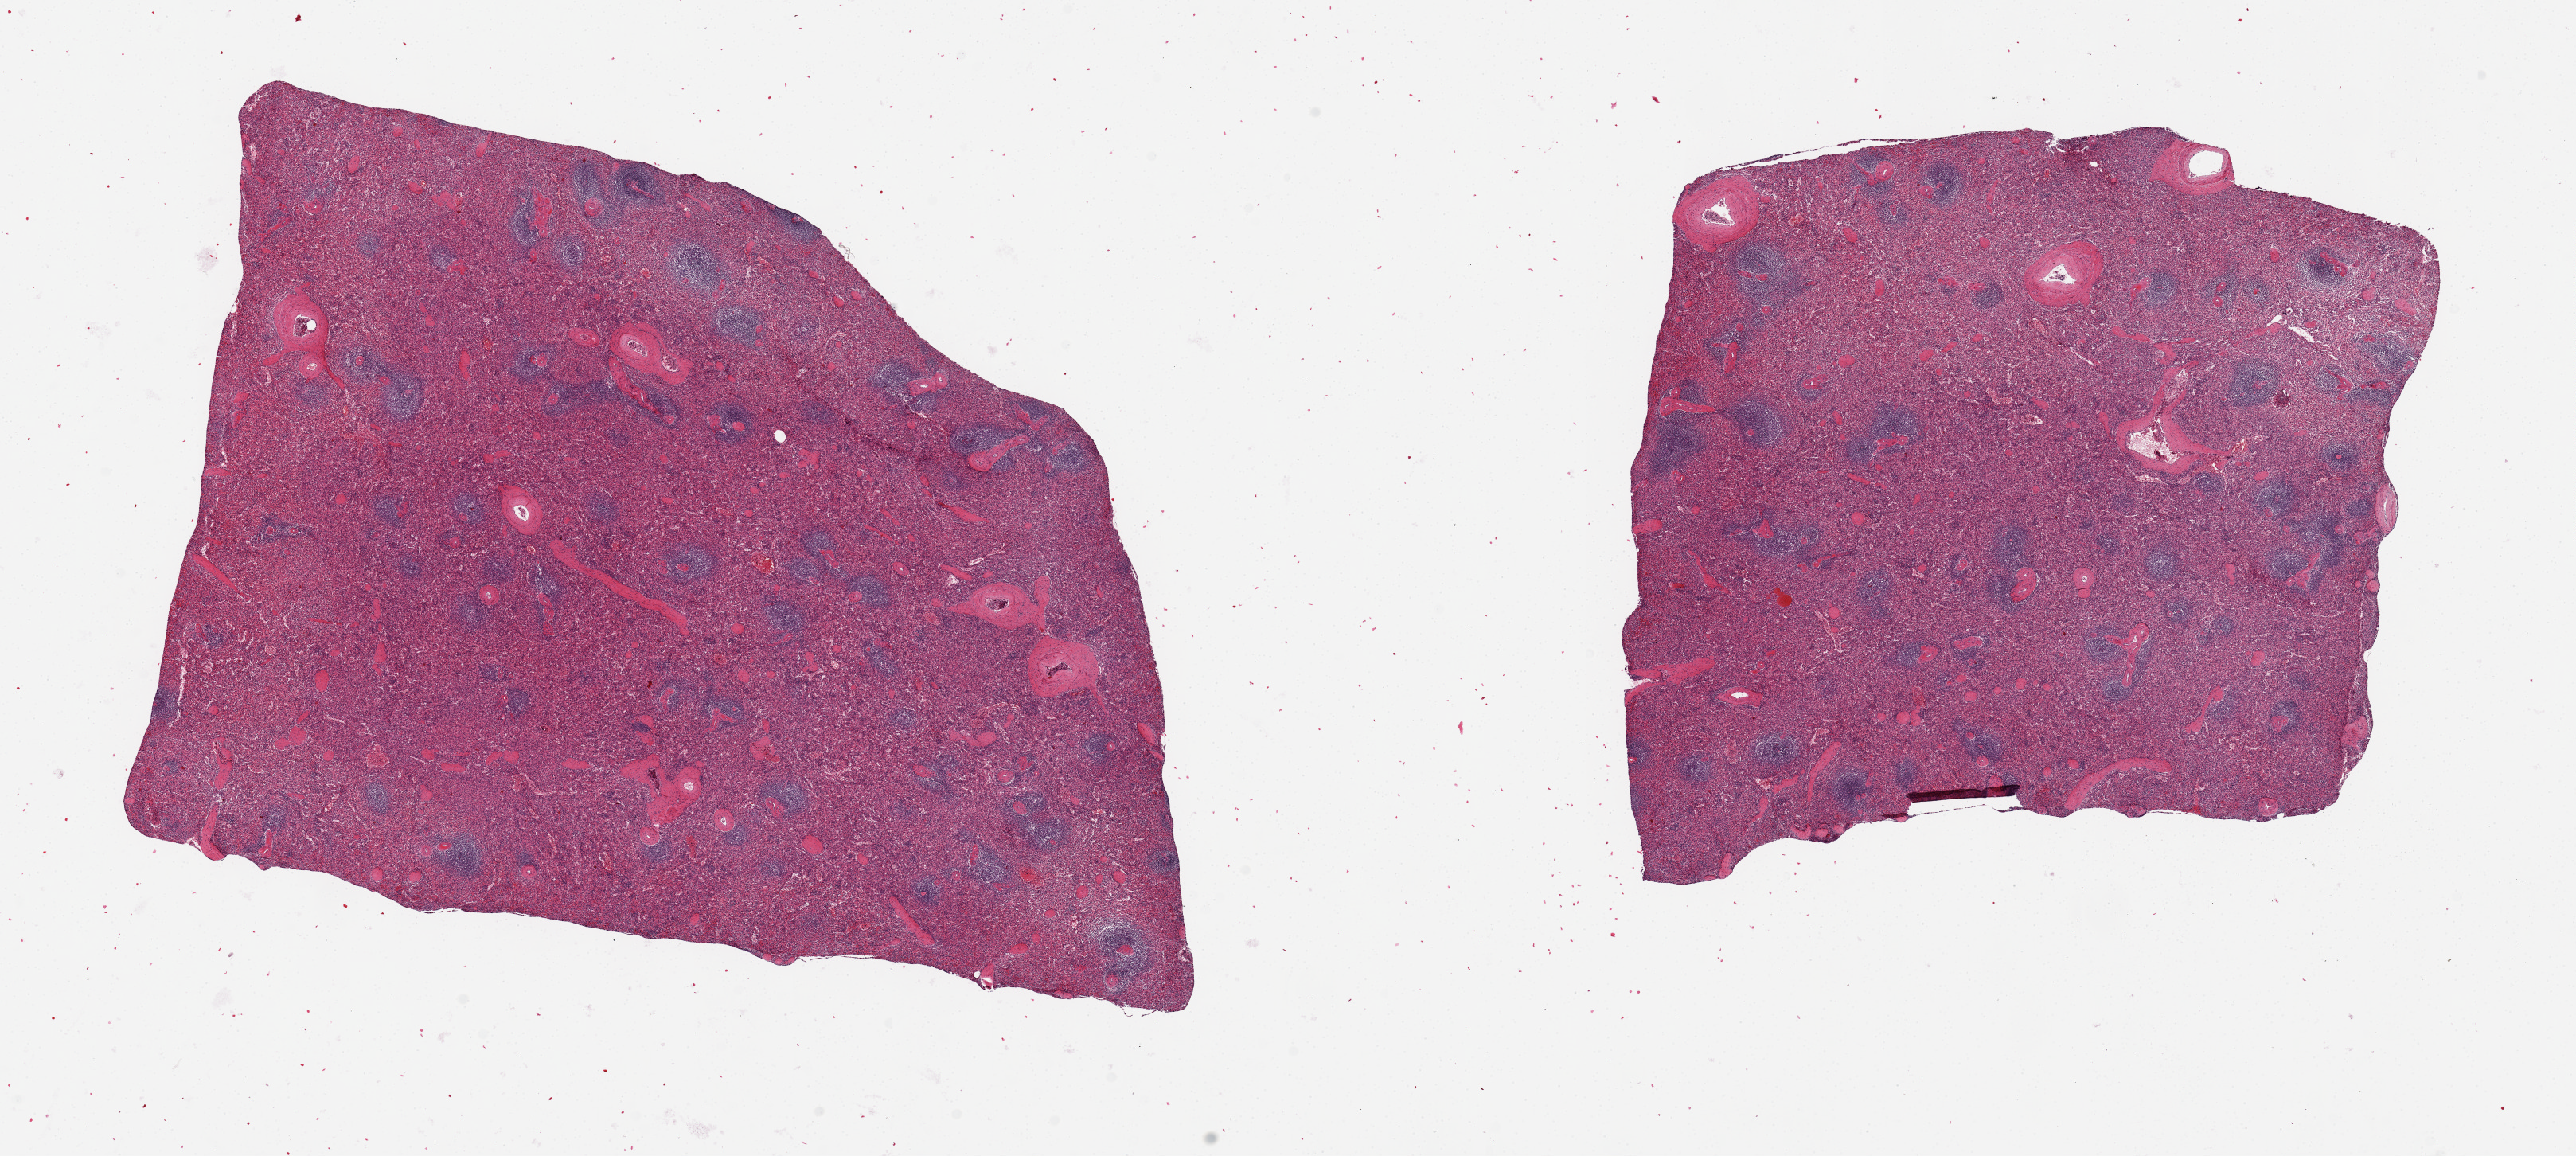
Hematoxylin and eosin (H&E) whole-slide image — shown as a low-resolution overview of the whole scanned area (about 25.6 x 11.5 mm), PAXgene-fixed, paraffin-embedded tissue, sampled site (target tissue): spleen, tissue donor sample. Donor sex: male.
* pathologist's review note for this sample: 2 pieces, 11x7.5 and 7.5x7mm; slight congestion